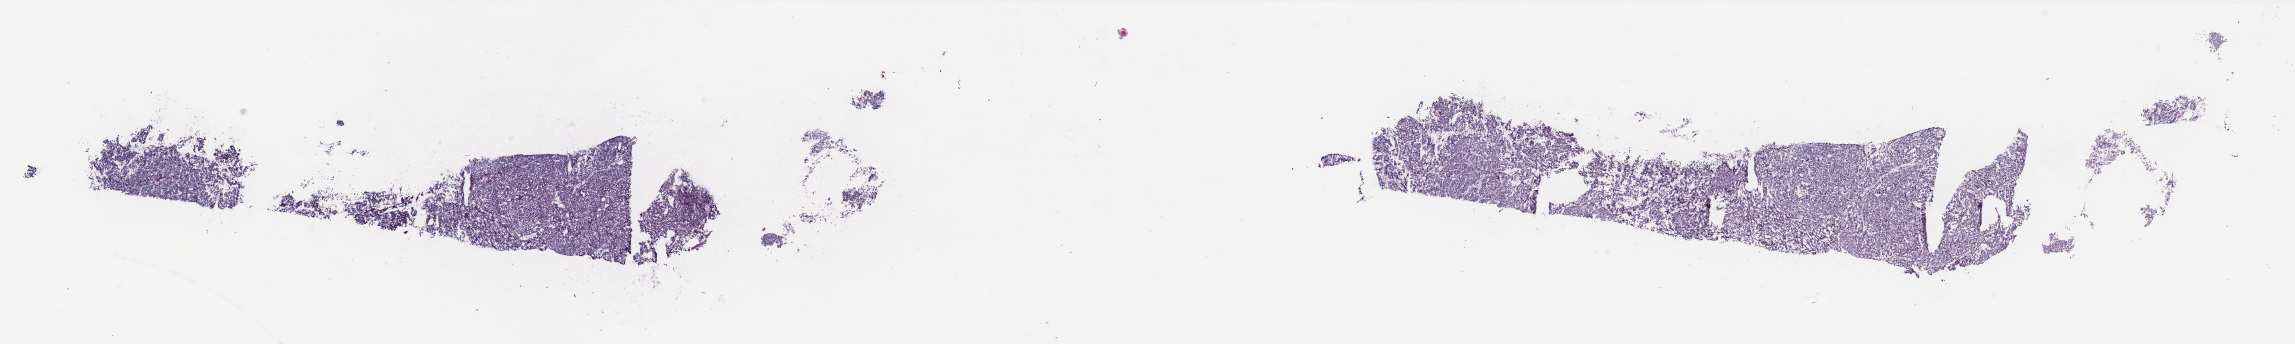
Digitized H&E tissue section (whole slide) — shown as a low-resolution overview of the whole scanned area (about 36.8 x 5.5 mm, from a 40x scan); frozen section; primary tumour sample from the uterus. Female, age 60 years at initial diagnosis. Histologic grade: G3 (poorly differentiated). Slide review estimates, as recorded: tumour cells 100%, tumour nuclei 90%, normal cells 0%, stromal cells 0%, necrosis 0%. Inflammatory infiltration, as recorded: lymphocyte infiltration 0%, monocyte infiltration 0%, neutrophil infiltration 0%.
Diagnosis: Endometrioid adenocarcinoma, NOS (endometrium). FIGO stage: IA. Lymph nodes positive (case pathology): 0 of 14 examined.